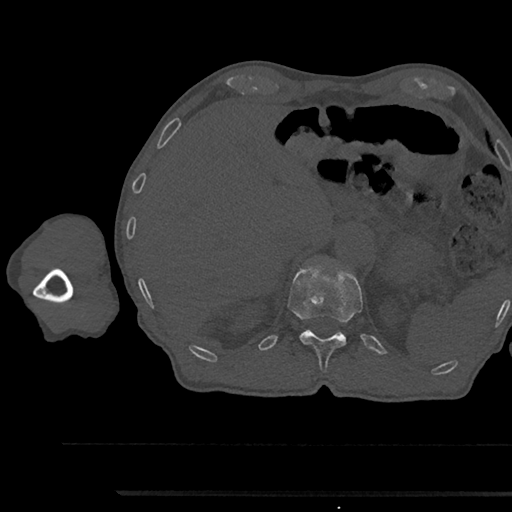
CT including the spine, one axial slice. Reconstruction kernel Br40s/3. 120 kVp. Bone window (W 1800 / L 400 HU). 0.5 mm slice thickness. 512 × 512 image matrix. Patient: male, 79 years. From the clinical record (not read from this slice): primary cancer: prostate.
Structures marked on this image (semi-automatic segmentation, software-assisted and operator-edited):
- T12 vertebra: bounding box [x1, y1, x2, y2] px = [288, 267, 362, 371]